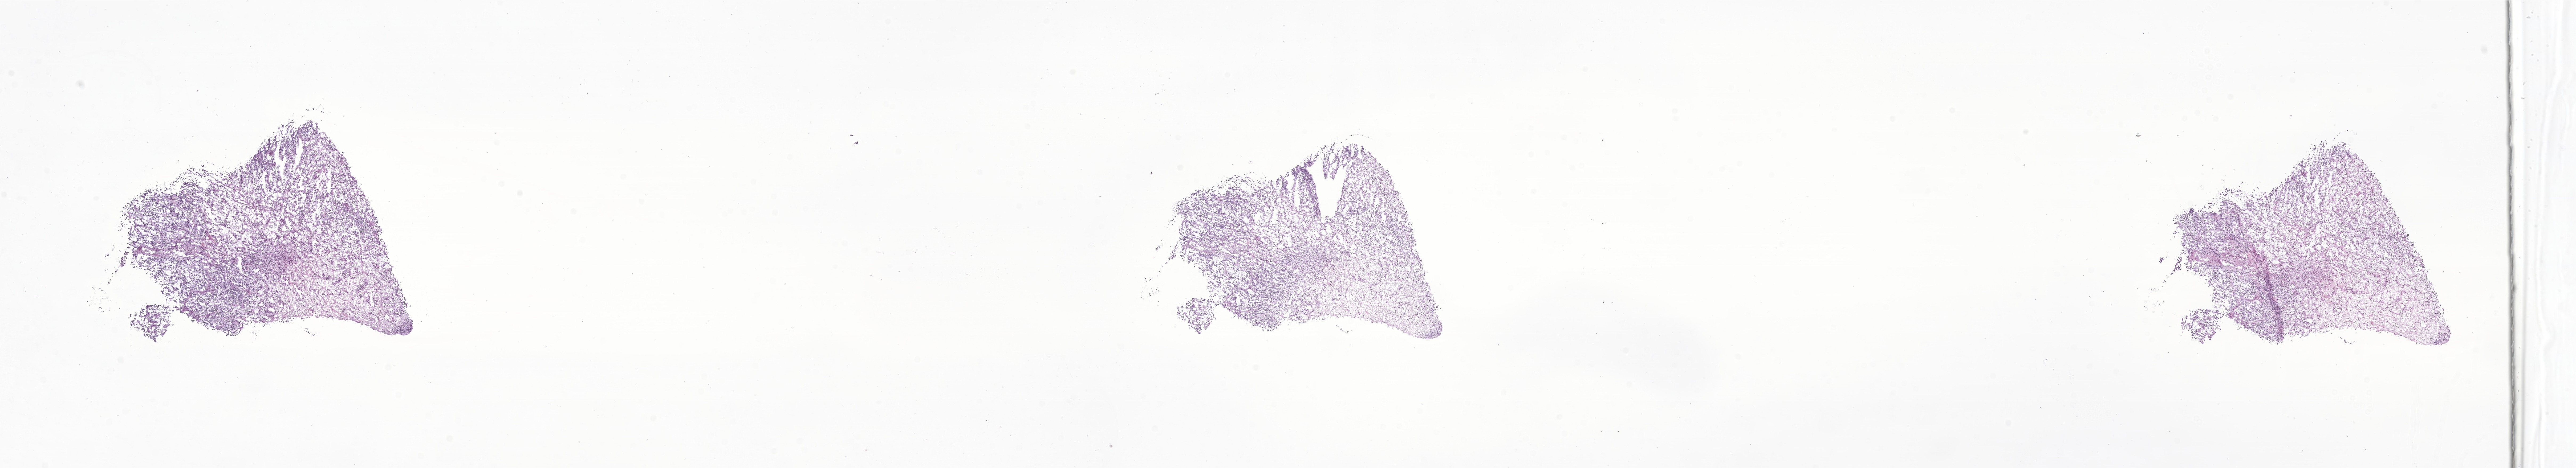
Whole-slide image, H&E stain of tumor tissue from the head and neck — shown as a low-resolution overview of the whole scanned area (about 40.8 x 7.4 mm); frozen section. Patient male; age 190 months.
Diagnosis: Rhabdomyosarcoma, NOS. Tissue or organ of origin (case record): head, face or neck.